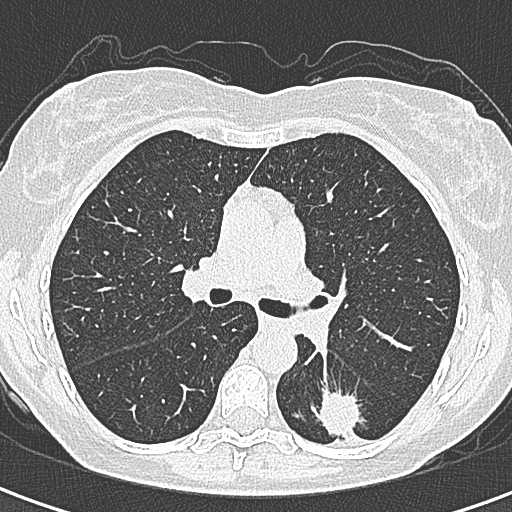
Low-dose screening chest CT, axial slice; baseline annual screen; lung window (W 1500 / L -600 HU); 1 mm slice thickness; lung (sharp) reconstruction kernel (B80f); slice 125 of 328 in the series; 512 × 512 image matrix, field of view 284 × 284 mm. Female, age 58 years at enrolment. Former smoker at enrolment.
Lesion marked by an expert reader, bounding box <293,389,363,455> (left, top, right, bottom; pixels). The screening reader recorded 2 non-calcified nodules or masses ≥4 mm on this exam (left lower lobe, right lower lobe); which of them this box marks is not recorded.